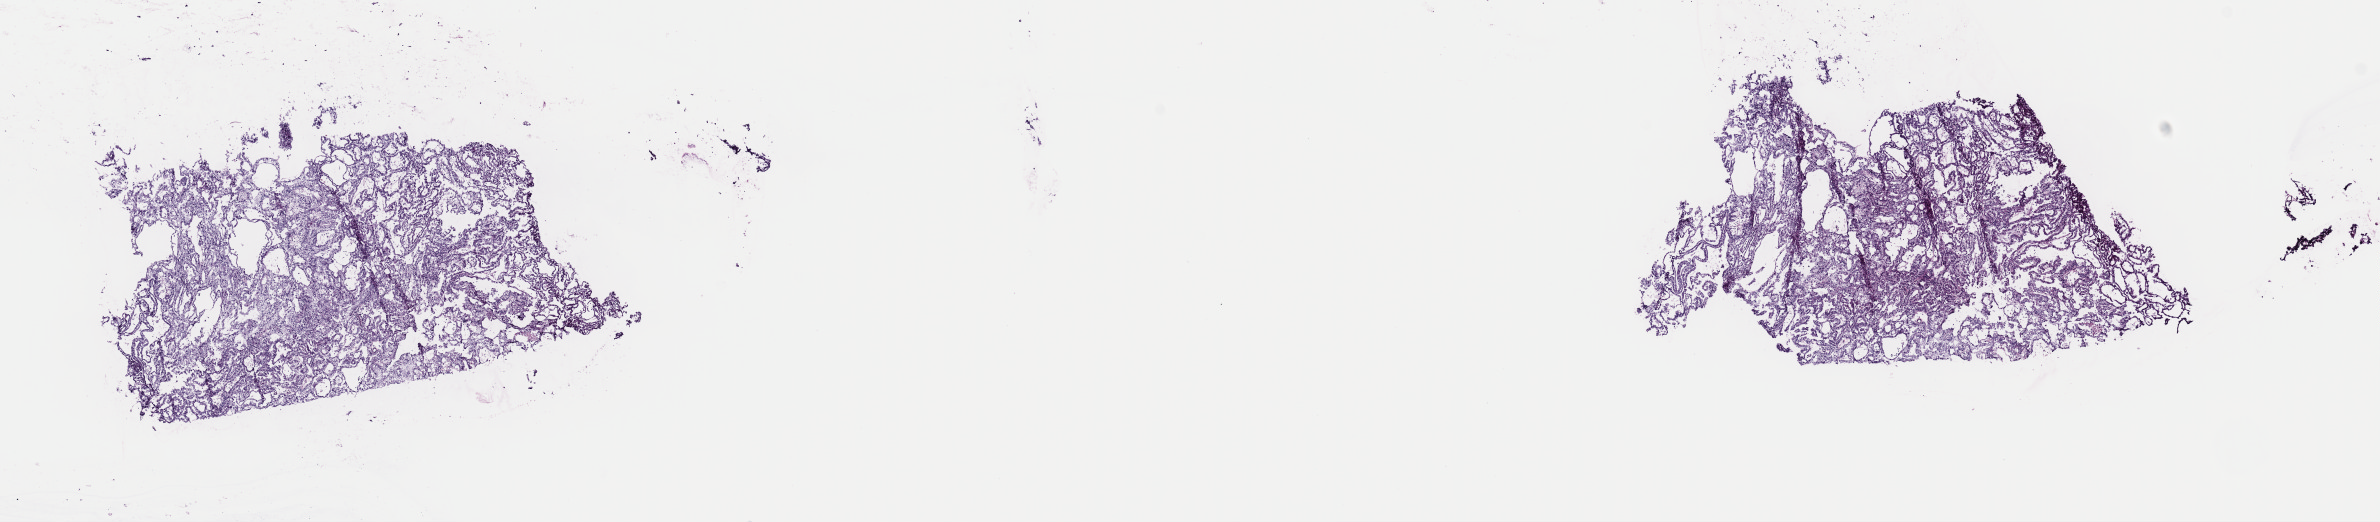
Whole-slide histology image, H&E-stained, shown as a low-resolution overview of the whole scanned area (about 18.8 x 4.1 mm, from a 40x scan), frozen section from the top of the tissue portion, primary tumour sample from the kidney. Patient: male, age at initial diagnosis 43 years. Slide review estimates, as recorded: tumour cells 93%, tumour nuclei 93%, normal cells 0%, stromal cells 5%, necrosis 2%. Inflammatory infiltration, as recorded: lymphocyte infiltration 2%, monocyte infiltration 4%, neutrophil infiltration 0%.
* AJCC pathologic stage: I
* pathologic diagnosis: Papillary adenocarcinoma, NOS